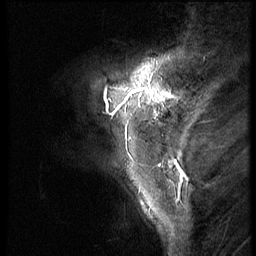
Breast MRI (dynamic contrast-enhanced), one sagittal slice; slice 12 of 56 in the series (ordered by position); 3 images stored at this slice position (order not interpretable as contrast timing); 1.5 T; TE 4.2 ms, TR 9 ms; 256 × 256 image matrix, field of view 180 × 180 mm. Patient: female, 46 years. Case-level facts recorded for this patient, not image findings: setting: breast cancer imaged before/during neoadjuvant chemotherapy; receptor status: HER2-positive.
Outlined on this slice (semi-automatic segmentation, software-assisted and operator-edited):
- analysis volume of interest (the breast-tissue region the enhancement analysis was run in; not a lesion): bounding box [x1, y1, x2, y2] px = [82, 68, 190, 143]
- tumour enhancement mask (voxels above the 140 % enhancement threshold inside the analysis volume of interest): [104, 81, 168, 115]